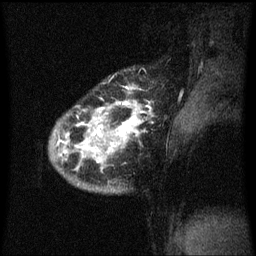
Breast MRI (dynamic contrast-enhanced), one sagittal slice. Position 51 of 60 along the scan axis. Dynamic contrast-enhanced series, image 2 of 3 at this slice position (ordered by acquisition). 1.5 T. TE 4.2 ms, TR 8.4 ms. 2 mm slice thickness. 256 × 256 image matrix, field of view 200 × 200 mm. Female patient, age 34 years. Case-level facts recorded for this patient, not image findings: setting: breast cancer imaged before/during neoadjuvant chemotherapy; receptor status: HR-positive, HER2-negative.
Annotated regions visible in this slice (semi-automatic segmentation, software-assisted and operator-edited):
- analysis volume of interest (the breast-tissue region the enhancement analysis was run in; not a lesion): box from (x=50, y=68) to (x=157, y=195) px
- tumour enhancement mask (voxels above the 70 % enhancement threshold inside the analysis volume of interest): (x=56, y=102)–(x=151, y=163)